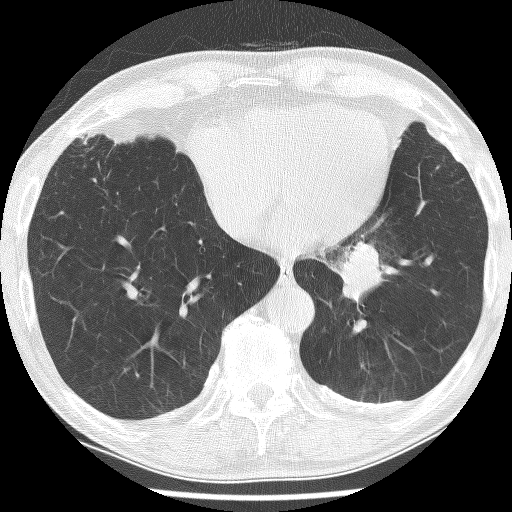
Chest CT (low-dose screening protocol), one axial image. First (baseline) screen. Lung window (W 1500 / L -600 HU). 2.5 mm slice thickness. Lung (sharp) reconstruction kernel (BONE). 512 × 512 image matrix. Male participant, aged 74 years at enrolment. Current smoker at enrolment.
• Expert reader's lesion annotation, bounding box (x1, y1, x2, y2) in pixels: (316, 226, 422, 319).
• Screening reader's record for this exam (one nodule recorded; not confirmed to be the boxed lesion): non-calcified nodule or mass ≥4 mm, left lower lobe, 30 × 27 mm, spiculated (stellate) margins, soft tissue attenuation.
• Later outcome: lung cancer diagnosed 151 days after this screen — adenocarcinoma, NOS, left lower lobe, stage IIIA (AJCC 6th edition), 49 mm at pathology.